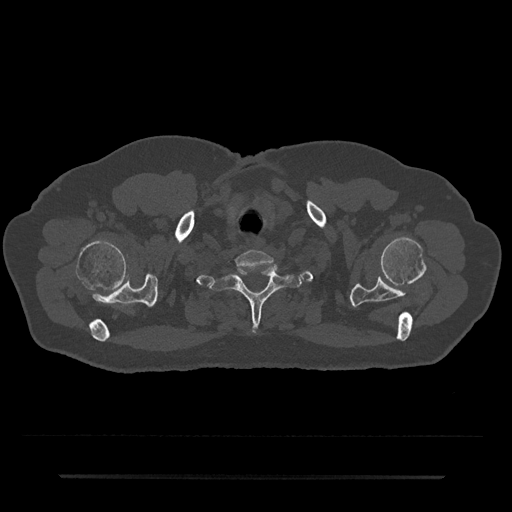
CT including the spine, one axial slice. Position 646 of 797 along the scan axis. Bone window (W 1800 / L 400 HU). 0.5 mm slice thickness. 512 × 512 image matrix, field of view 437 × 437 mm. Patient: male, 69 years. From the clinical record (not read from this slice): primary cancer: prostate.
Annotated regions visible in this slice (semi-automatically segmented with operator editing):
- T1 vertebra: bounding box [x1, y1, x2, y2] px = [210, 266, 302, 325]